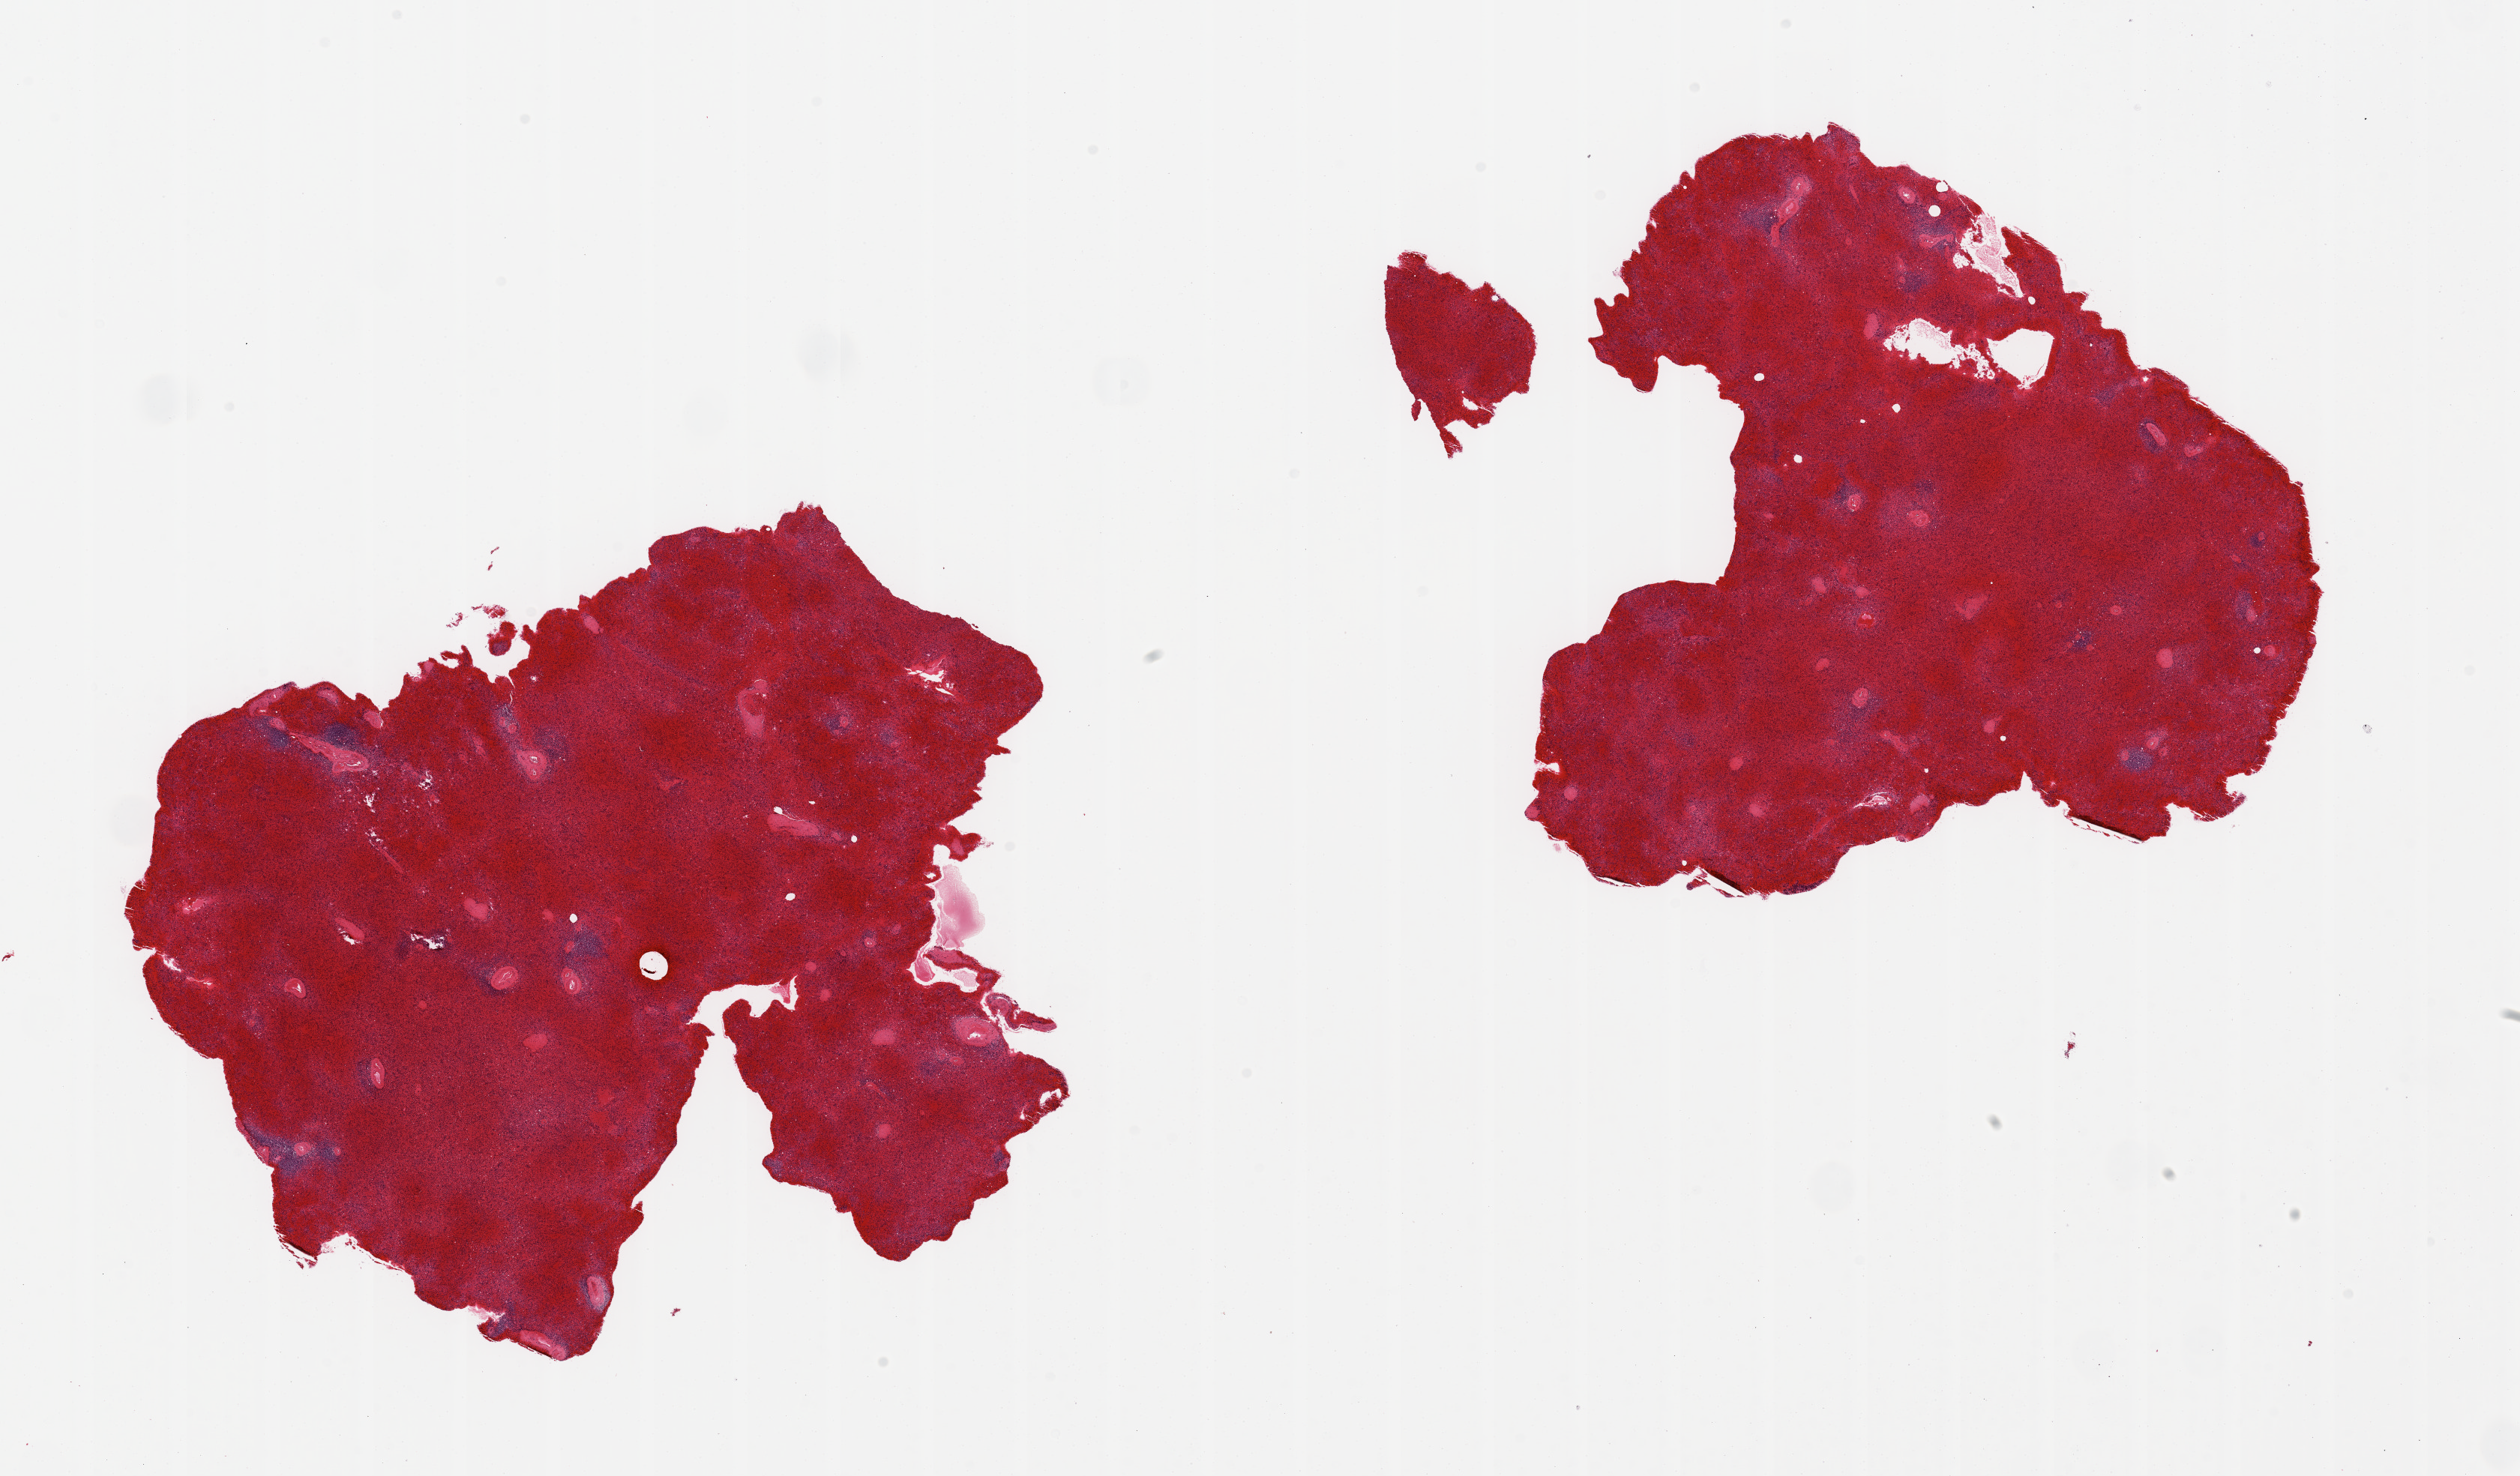
H&E whole-slide image — shown as a low-resolution overview of the whole scanned area (about 26.6 x 15.6 mm, acquisition: 20x scan). PAXgene-fixed, paraffin-embedded tissue. Sampled site (target tissue): spleen. Donor tissue sample.
- pathologist's review note for this sample: 2 pieces; severe vascular congestion